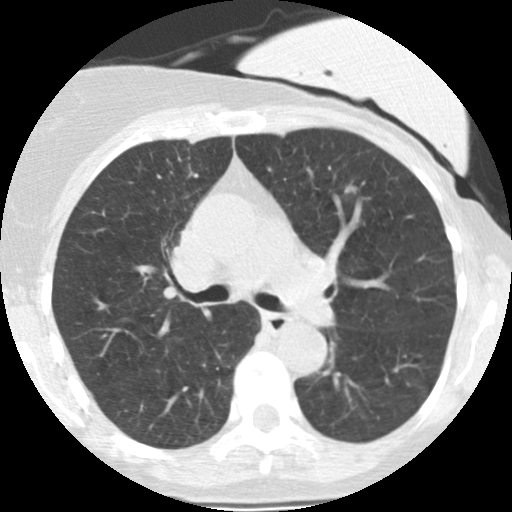
Low-dose screening chest CT, axial slice. Second screening round (one year after baseline). Lung window (W 1500 / L -600 HU). 2.5 mm slice thickness. Slice 95 of 251 in the series. Female participant, aged 66 years at enrolment. Former smoker at enrolment.
Expert reader's lesion annotation, bounding box [x1, y1, x2, y2] px = [343, 181, 361, 202]. Screening reader's record for this exam (one nodule recorded; not confirmed to be the boxed lesion): non-calcified nodule or mass ≥4 mm, left upper lobe, 7 × 5 mm, smooth margins, soft tissue attenuation, pre-existing on the prior screen: yes; interval growth: yes. Later outcome: lung cancer diagnosed 218 days after this screen — adenocarcinoma, NOS, left lower lobe, poorly differentiated (G3), stage IA (AJCC 6th edition), 8 mm at pathology.